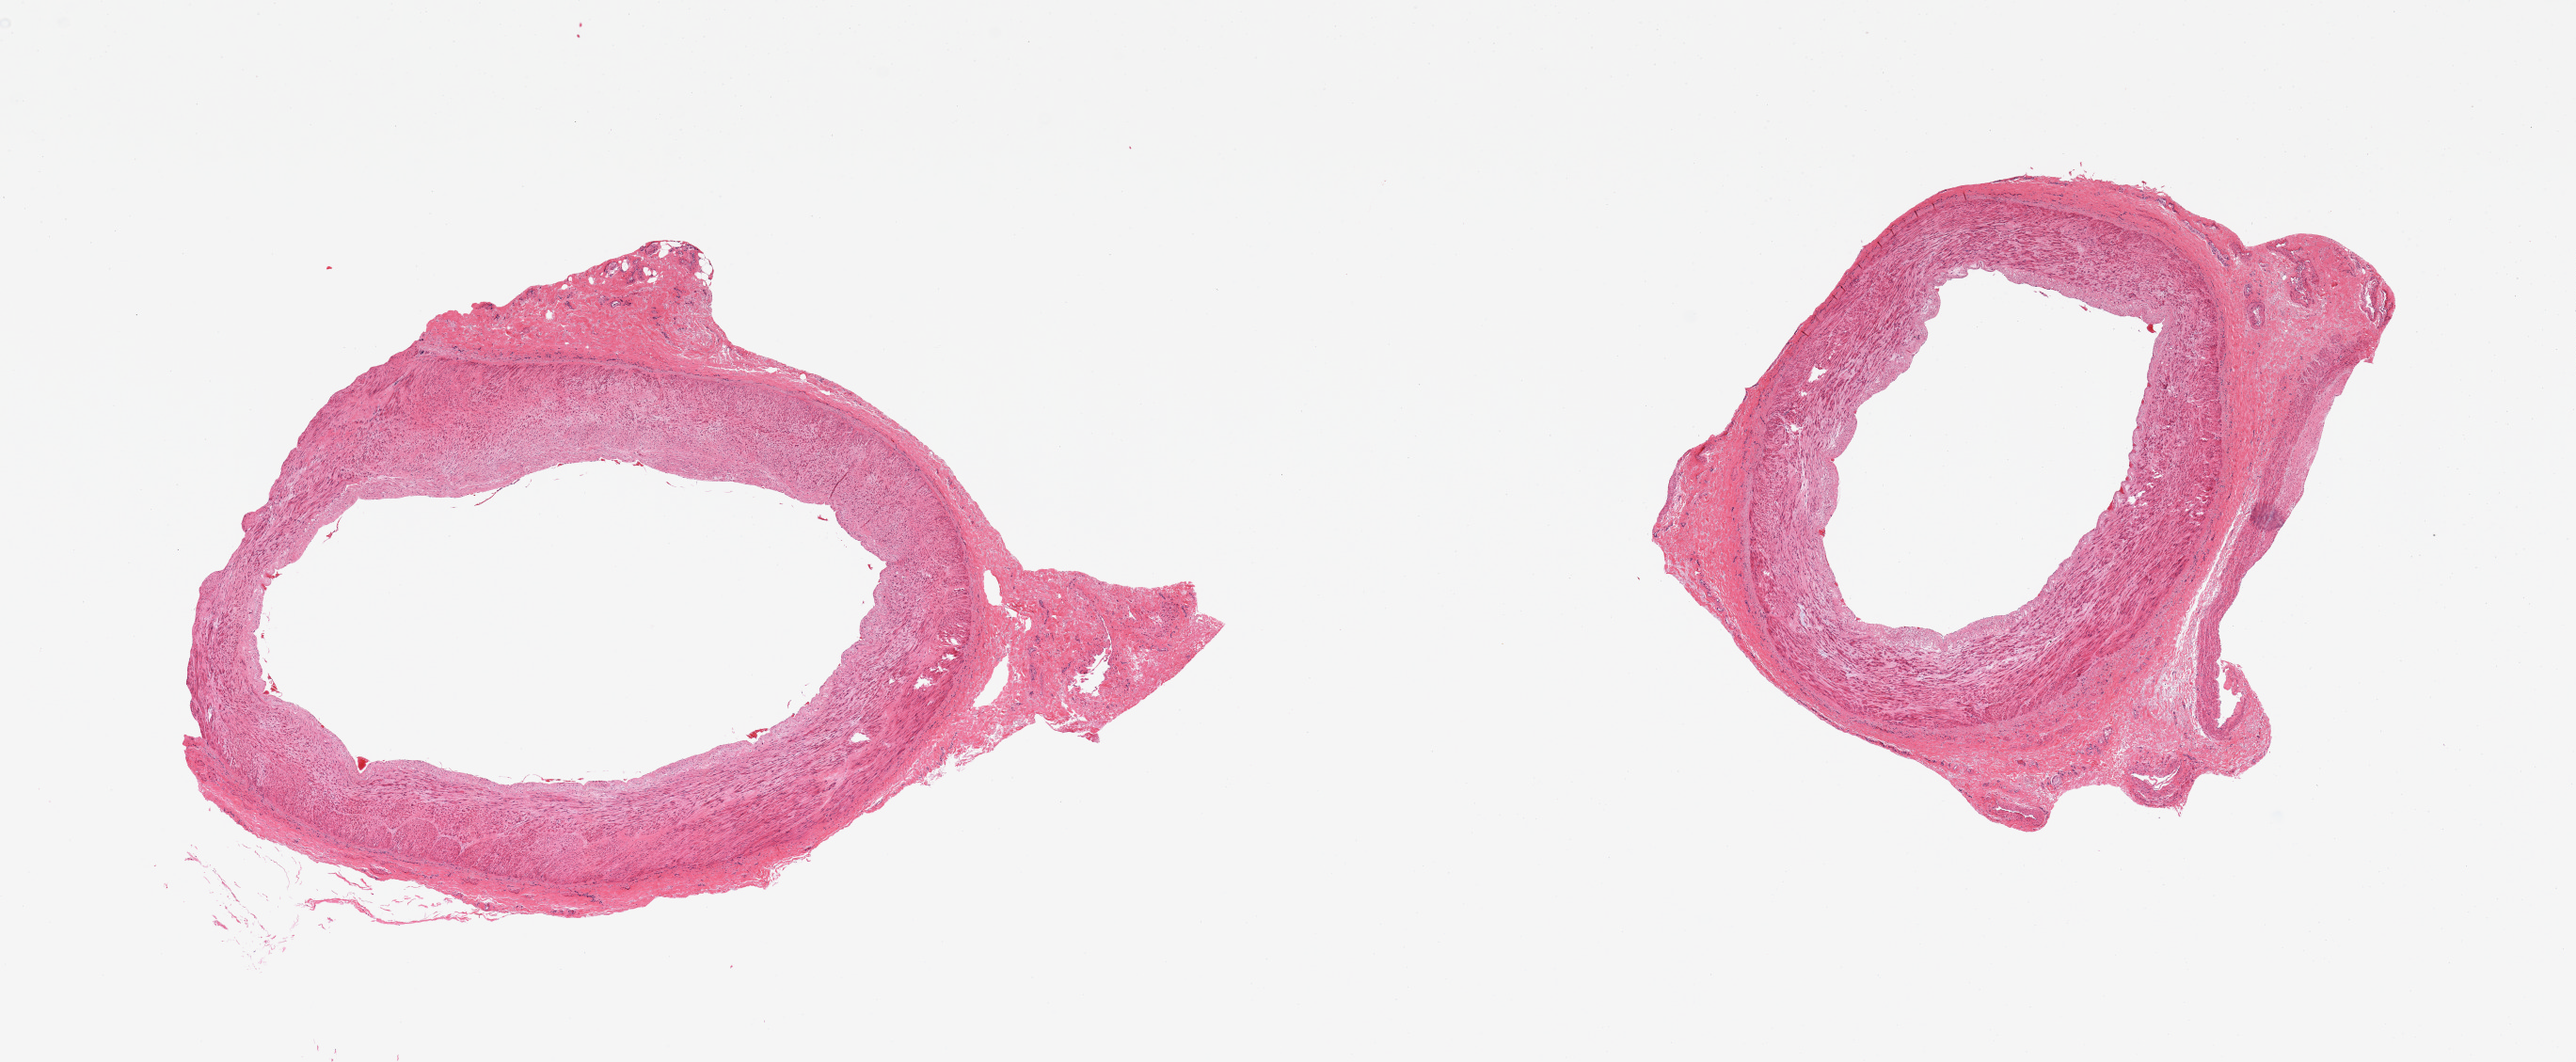
Hematoxylin and eosin (H&E) whole-slide image, shown as a low-resolution overview of the whole scanned area (about 21.7 x 8.9 mm, from a 20x scan), PAXgene-fixed, paraffin-embedded tissue, target tissue: tibial artery, tissue donor sample. Male donor.
• reviewer comment on this tissue sample: 2 pieces, adherent nubbins fibroconnective tissue on both